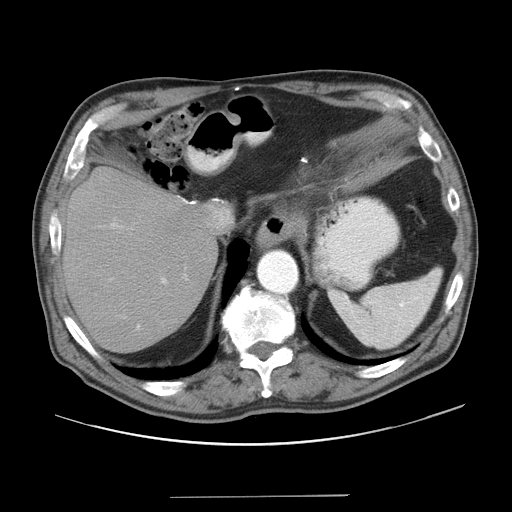
Contrast-enhanced abdominal CT, one axial slice. Position 32 of 41 along the scan axis. Reconstruction kernel STANDARD. 120 kVp. Intravenous contrast given. Soft-tissue window (W 400 / L 40 HU). 5 mm slice thickness. 512 × 512 image matrix. Male patient, age 75 years. Case-level facts recorded for this patient, not image findings: diagnosis: colorectal cancer liver metastases, imaged before liver resection; multiple liver metastases: no; largest metastasis: 5.2 cm.
Structures marked on this image (expert manual segmentation):
- hepatic veins: bounding box <209,206,232,227> (left, top, right, bottom; pixels)
- liver: <65,170,217,352>
- planned liver remnant (the part of the liver to remain after resection): <81,209,217,352>
- portal vein (with intrahepatic branches): <98,222,167,330>